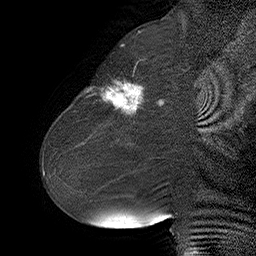
Breast MRI (dynamic contrast-enhanced), one sagittal slice; position 23 of 55 along the scan axis; dynamic contrast-enhanced series, time point 2 of 6 at this slice position (early post-contrast); 1.5 T; TE 4.5 ms, TR 32.4 ms; 3 mm slice thickness; 256 × 256 image matrix, field of view 180 × 180 mm. Female patient. Case-level facts recorded for this patient, not image findings: setting: breast cancer imaged before/during neoadjuvant chemotherapy; receptor status: HER2-positive.
Outlined on this slice (semi-automatically segmented with operator editing):
- analysis volume of interest (the breast-tissue region the enhancement analysis was run in; not a lesion): bounding box (x1, y1, x2, y2) in pixels: (80, 64, 163, 134)
- tumour enhancement mask (voxels above the 100 % enhancement threshold inside the analysis volume of interest): (86, 82, 163, 115)